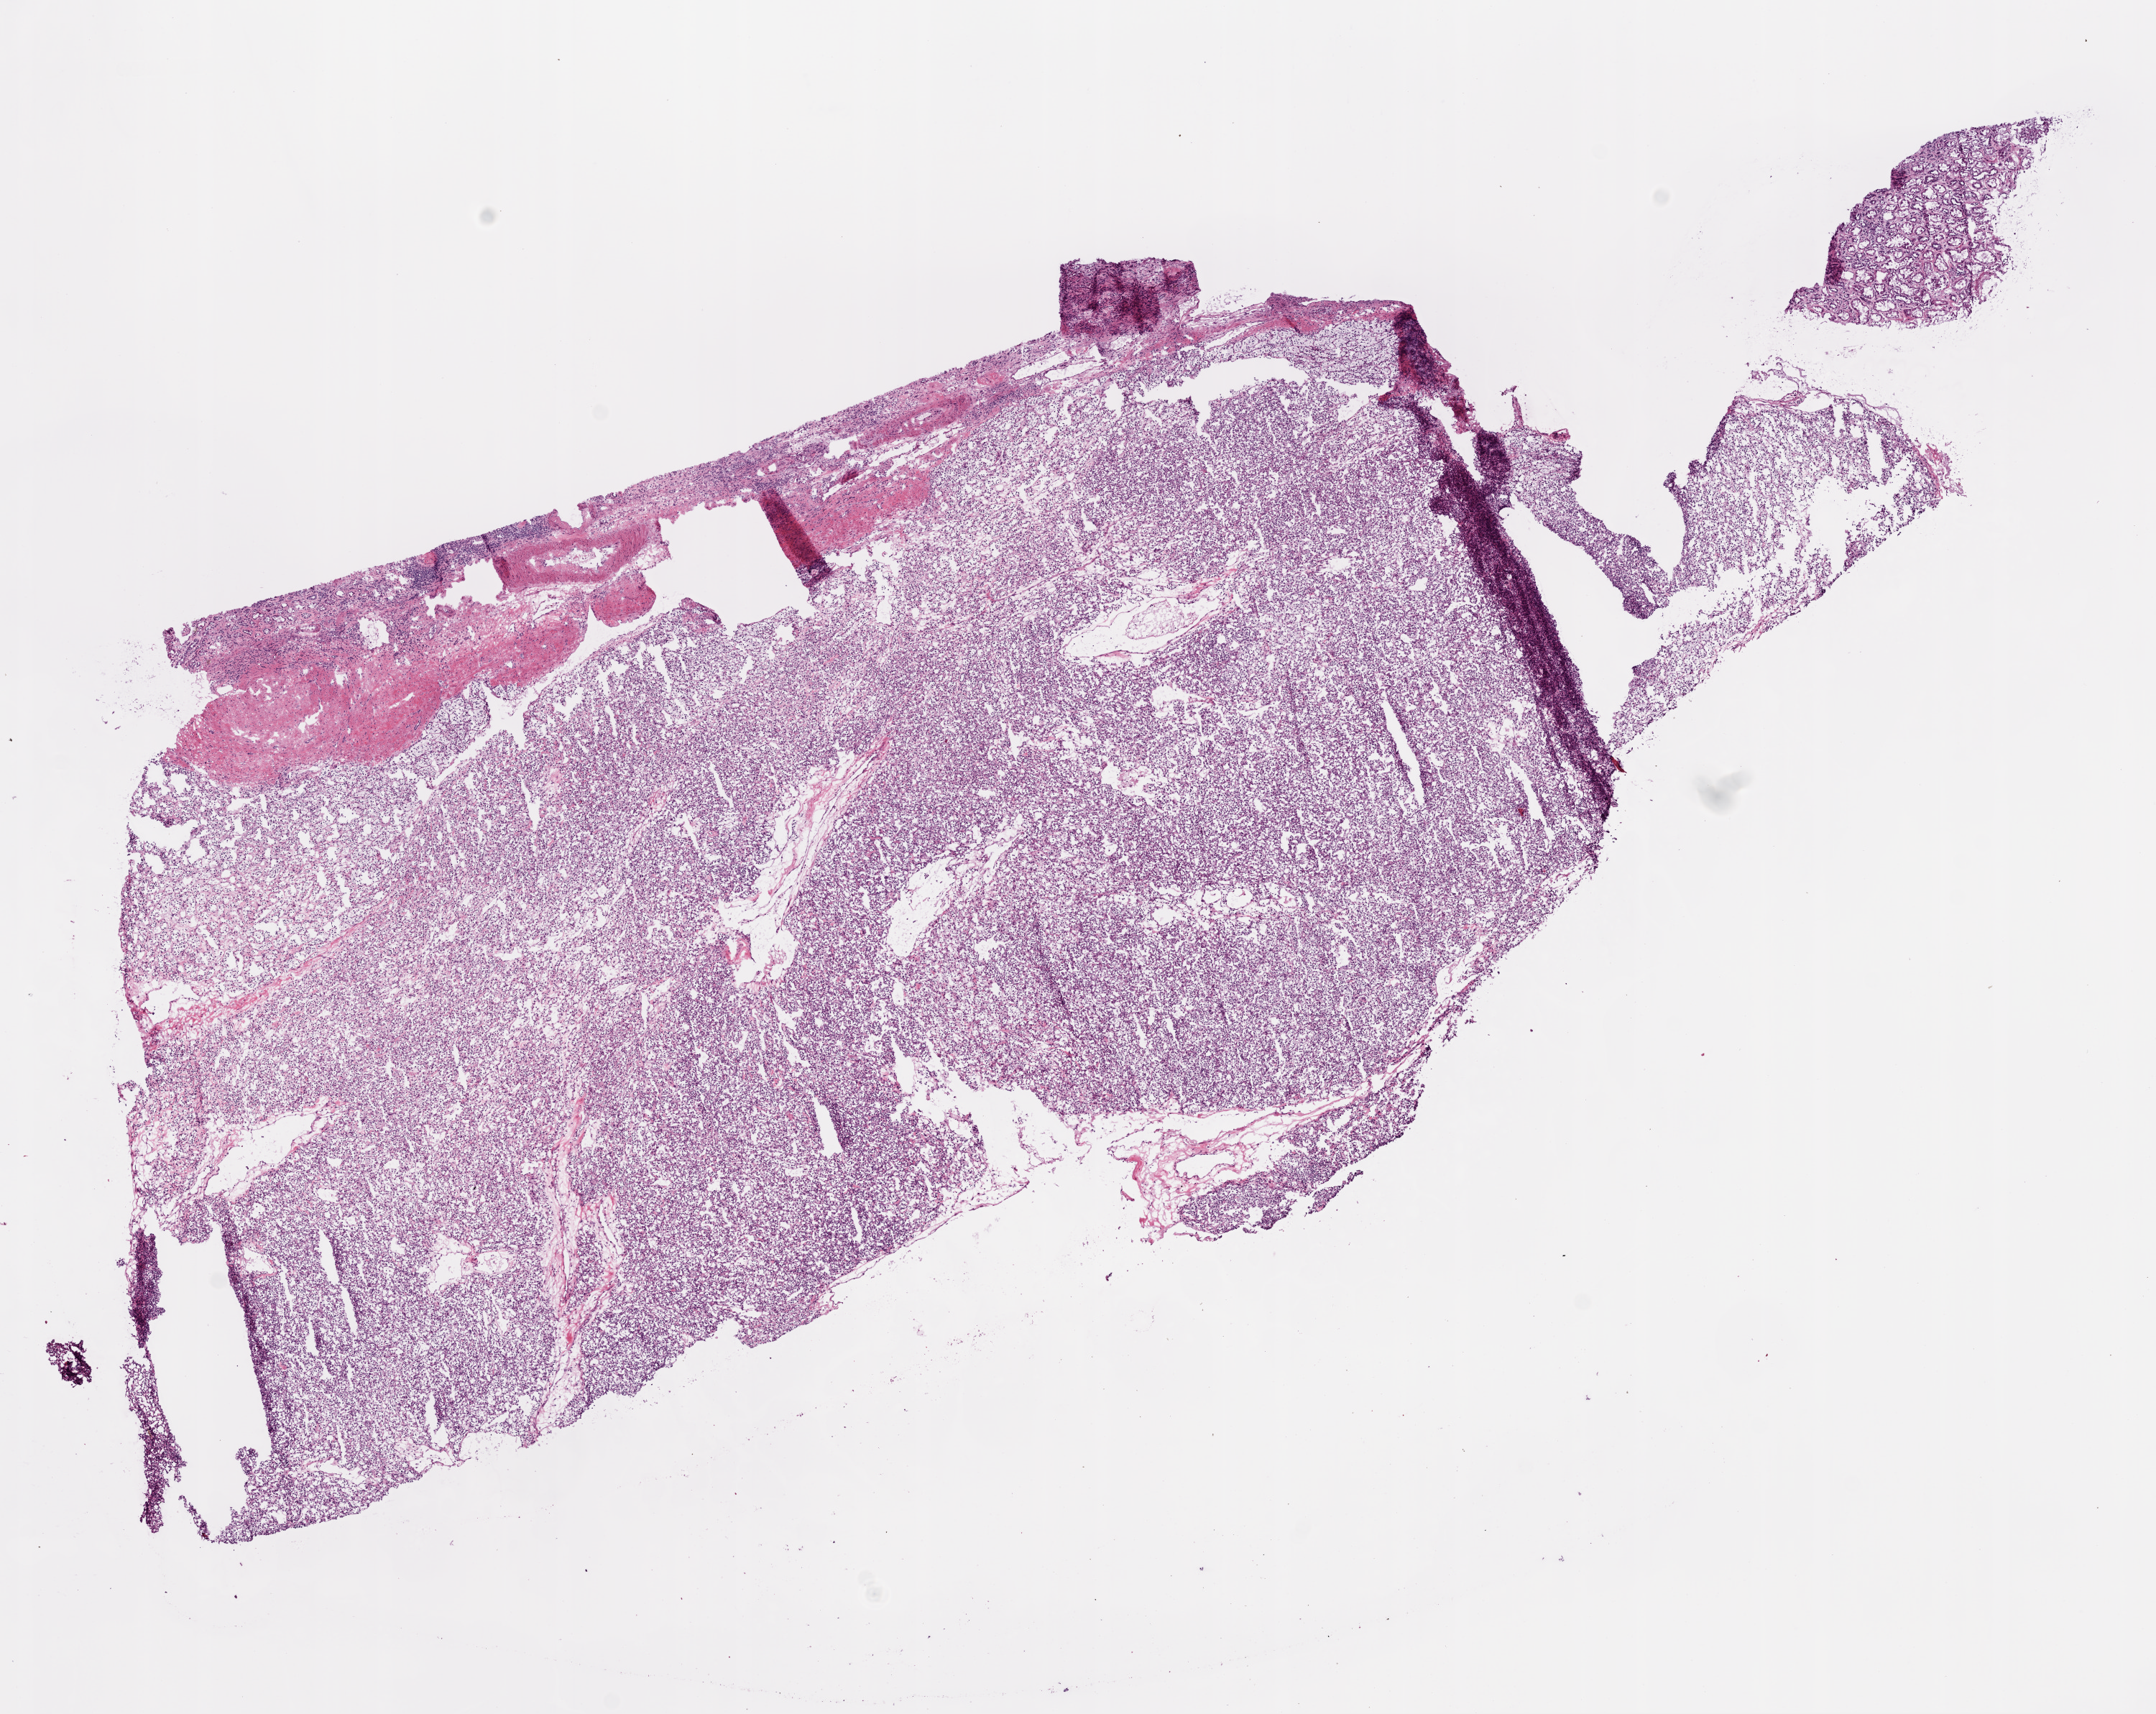
Digitized H&E-stained tissue section (whole slide), low-resolution overview of the scanned area, about 12.0 x 9.6 mm (acquisition: 20x scan); frozen section; primary tumour sample from the kidney. Patient: female, age at initial diagnosis 66 years. Histologic grade: G3 (poorly differentiated). Pathologist review of this section (percent, as recorded): tumour cells 90%, tumour nuclei 85%, normal cells 5%, stromal cells 5%, necrosis 0%.
Histologic diagnosis: Clear cell adenocarcinoma, NOS. AJCC pathologic stage: I.